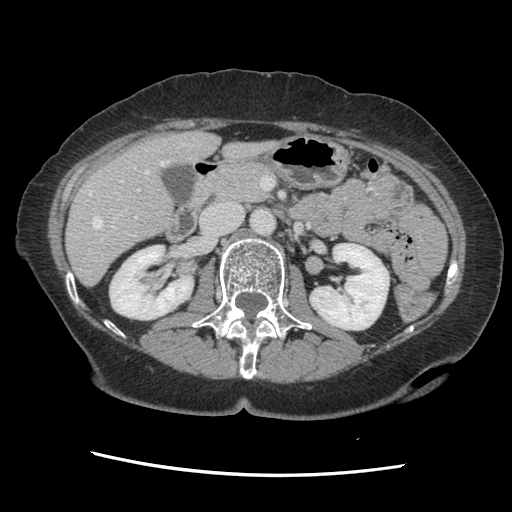
Contrast-enhanced abdominal CT, one axial slice; position 66 of 141 along the scan axis; 120 kVp; soft-tissue window (W 400 / L 40 HU); 2.5 mm slice thickness; 512 × 512 image matrix, field of view 330 × 330 mm. Female patient, age 61 years. From the clinical record (not read from this slice): diagnosis: colorectal cancer liver metastases, imaged before liver resection; multiple liver metastases: no; largest metastasis: 2.4 cm; disease in both lobes: no.
Outlined on this slice (manually delineated by an expert):
- hepatic veins: box from (x=89, y=160) to (x=169, y=229) px
- liver: (x=67, y=132)–(x=272, y=284)
- planned liver remnant (the part of the liver to remain after resection): (x=67, y=132)–(x=272, y=285)
- portal vein (with intrahepatic branches): (x=100, y=179)–(x=140, y=242)